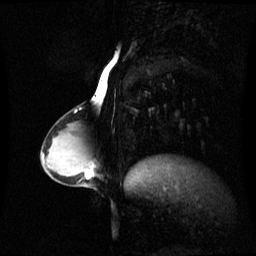
Breast MRI (dynamic contrast-enhanced), one sagittal slice. Slice 28 of 60 in the series (ordered by position). Dynamic contrast-enhanced series, image 2 of 3 at this slice position (ordered by acquisition). 1.5 T. TE 4.2 ms, TR 8.4 ms. 2.4 mm slice thickness. 256 × 256 image matrix. Female patient, age 34 years. From the clinical record (not read from this slice): setting: breast cancer imaged before/during neoadjuvant chemotherapy; receptor status: triple-negative.
Outlined on this slice (semi-automatically segmented with operator editing):
- analysis volume of interest (the breast-tissue region the enhancement analysis was run in; not a lesion): box from (x=57, y=156) to (x=93, y=187) px
- tumour enhancement mask (voxels above the 70 % enhancement threshold inside the analysis volume of interest): (x=85, y=170)–(x=93, y=177)